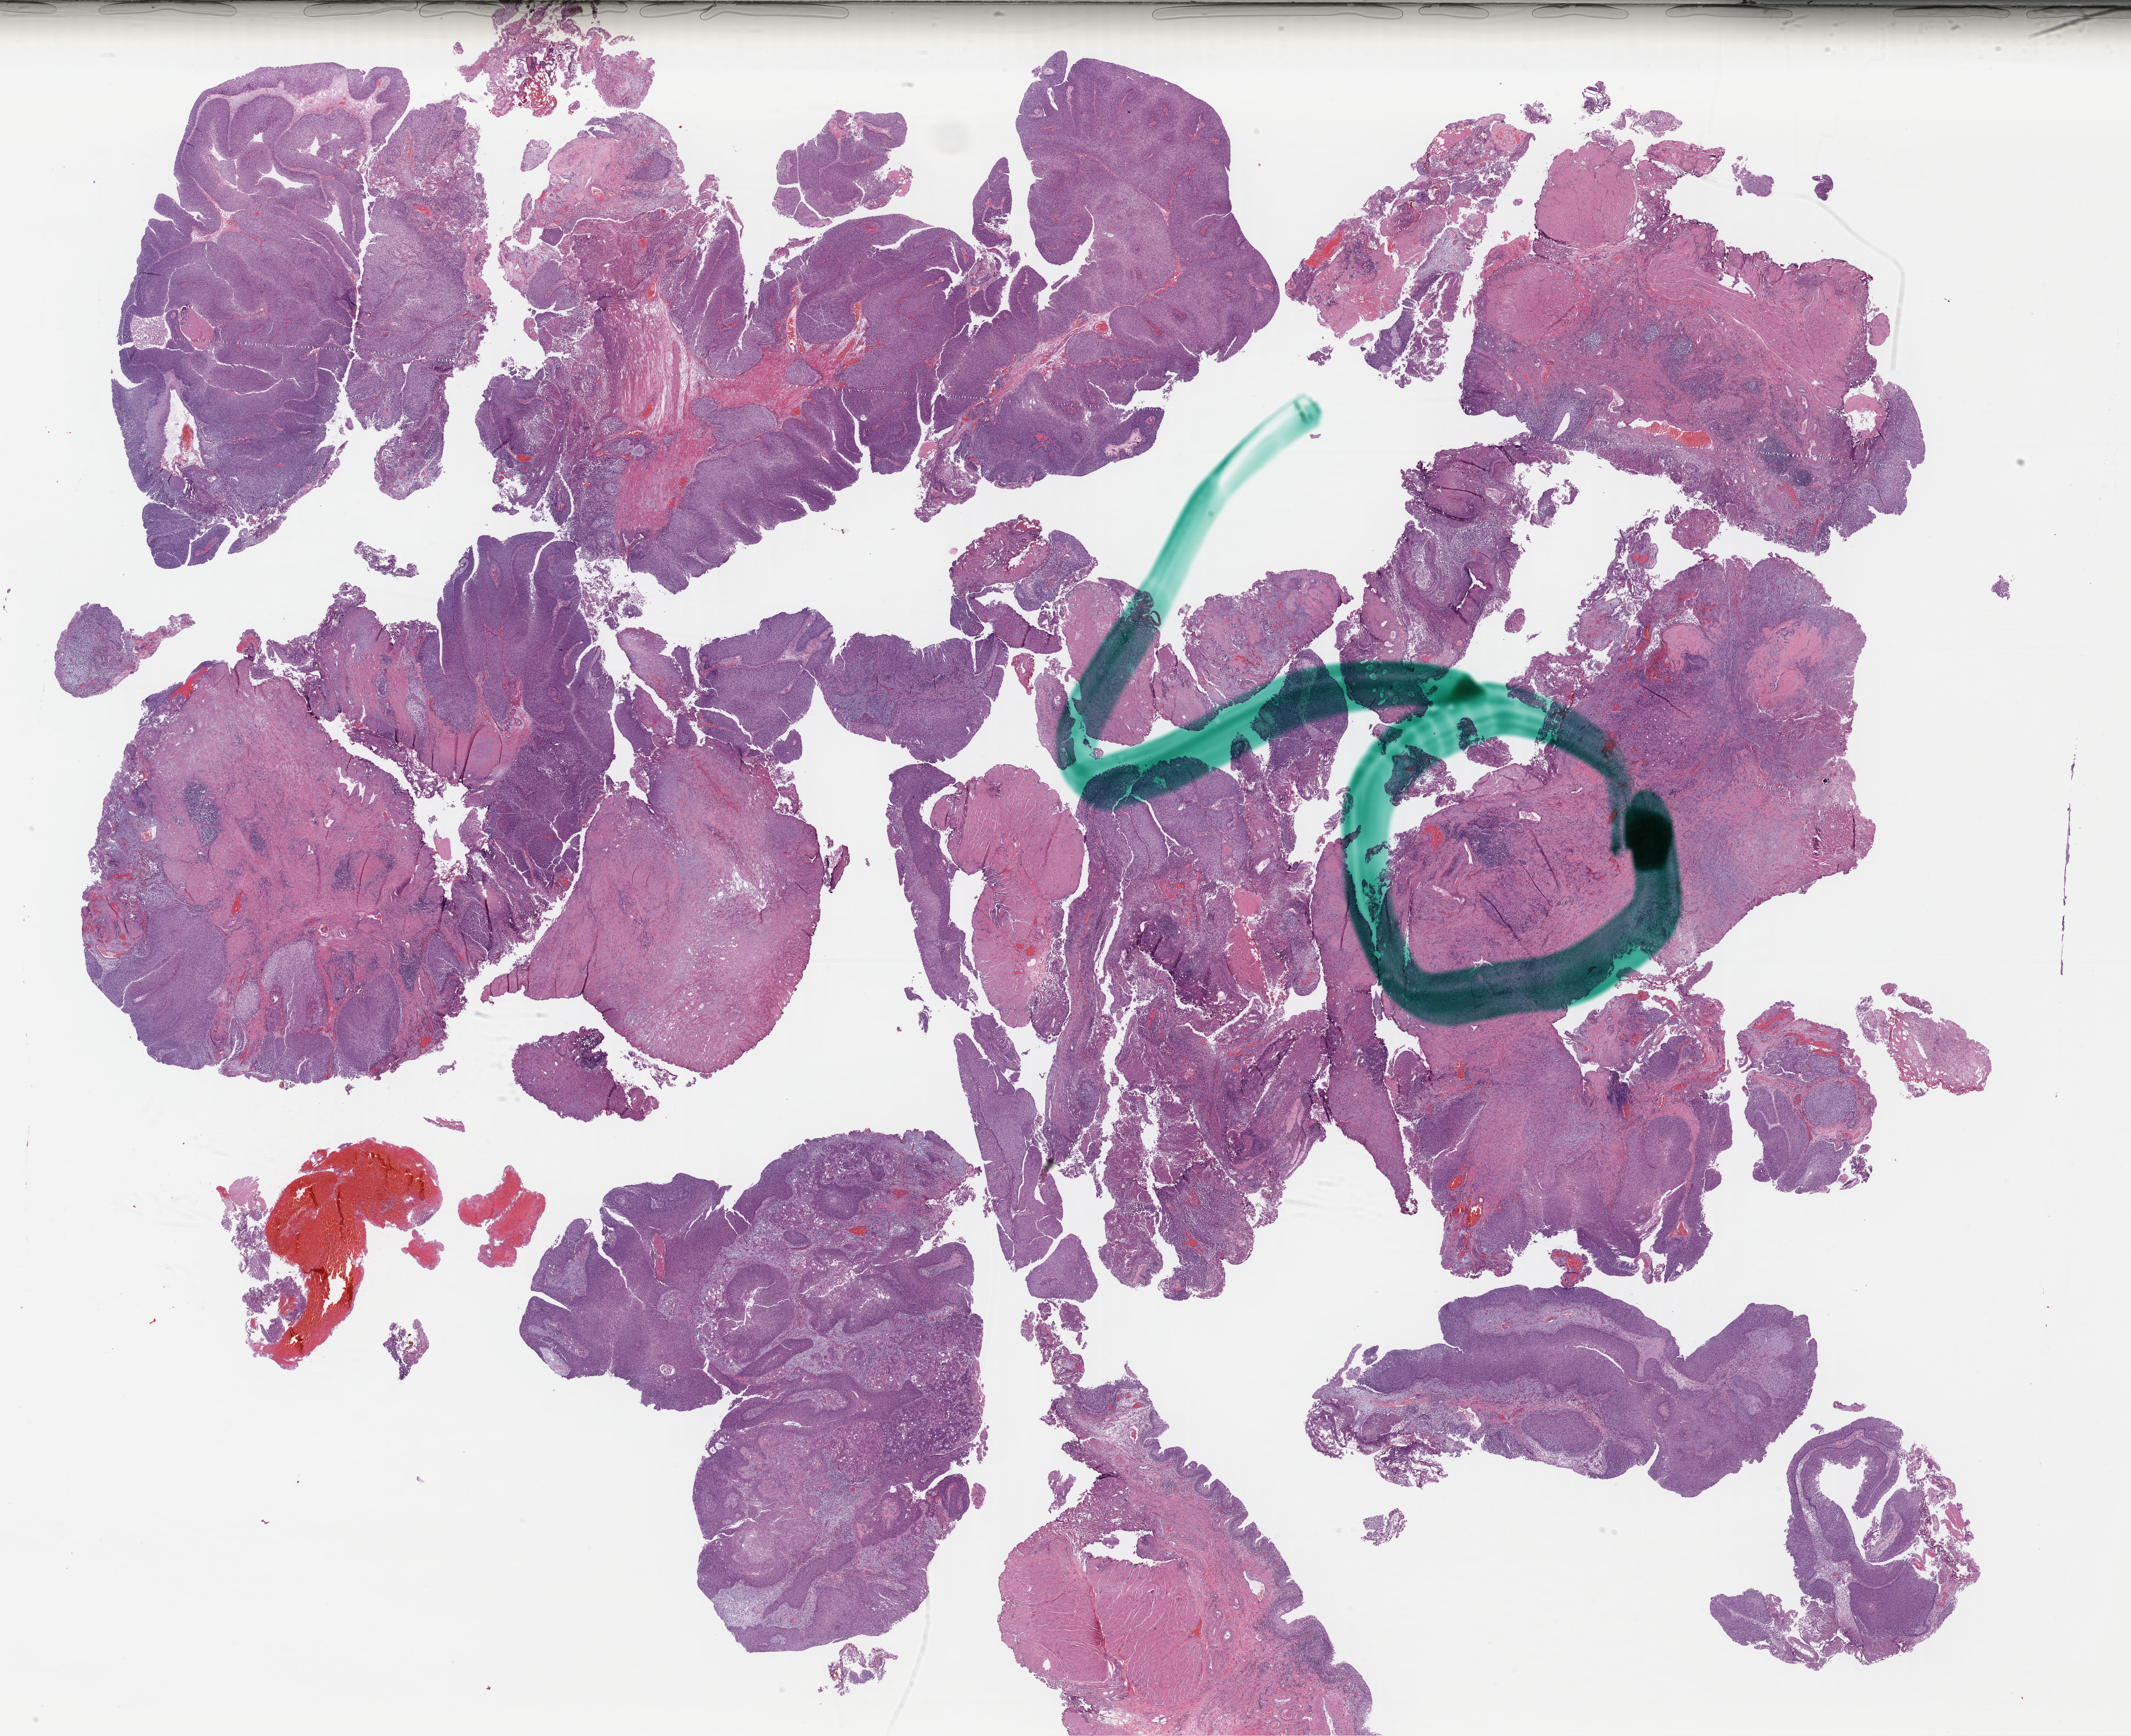
Whole-slide histology image, H&E, whole scanned area (about 28.5 x 23.2 mm) shown as a low-resolution overview. Formalin-fixed paraffin-embedded (FFPE) diagnostic section. Primary tumour sample from the bladder. Patient: male, age at initial diagnosis 72 years. Histologic grade: high grade.
Lymph nodes positive (case pathology): 0 of 29 examined. Histologic diagnosis: Papillary transitional cell carcinoma (lateral wall of bladder).